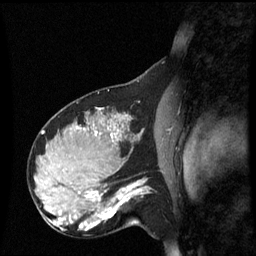
Breast MRI (dynamic contrast-enhanced), one sagittal slice. Slice 36 of 60 in the series (ordered by position). Dynamic contrast-enhanced series, image 2 of 3 at this slice position (ordered by acquisition). 1.5 T. TE 4.2 ms, TR 8.9 ms. 2.2 mm slice thickness. 256 × 256 image matrix. Patient: female, 31 years. Case-level facts recorded for this patient, not image findings: setting: breast cancer imaged before/during neoadjuvant chemotherapy; receptor status: HR-positive, HER2-negative.
Structures marked on this image (semi-automatic segmentation, software-assisted and operator-edited):
- analysis volume of interest (the breast-tissue region the enhancement analysis was run in; not a lesion): bounding box <90,180,151,229> (left, top, right, bottom; pixels)
- tumour enhancement mask (voxels above the 70 % enhancement threshold inside the analysis volume of interest): <90,182,143,227>